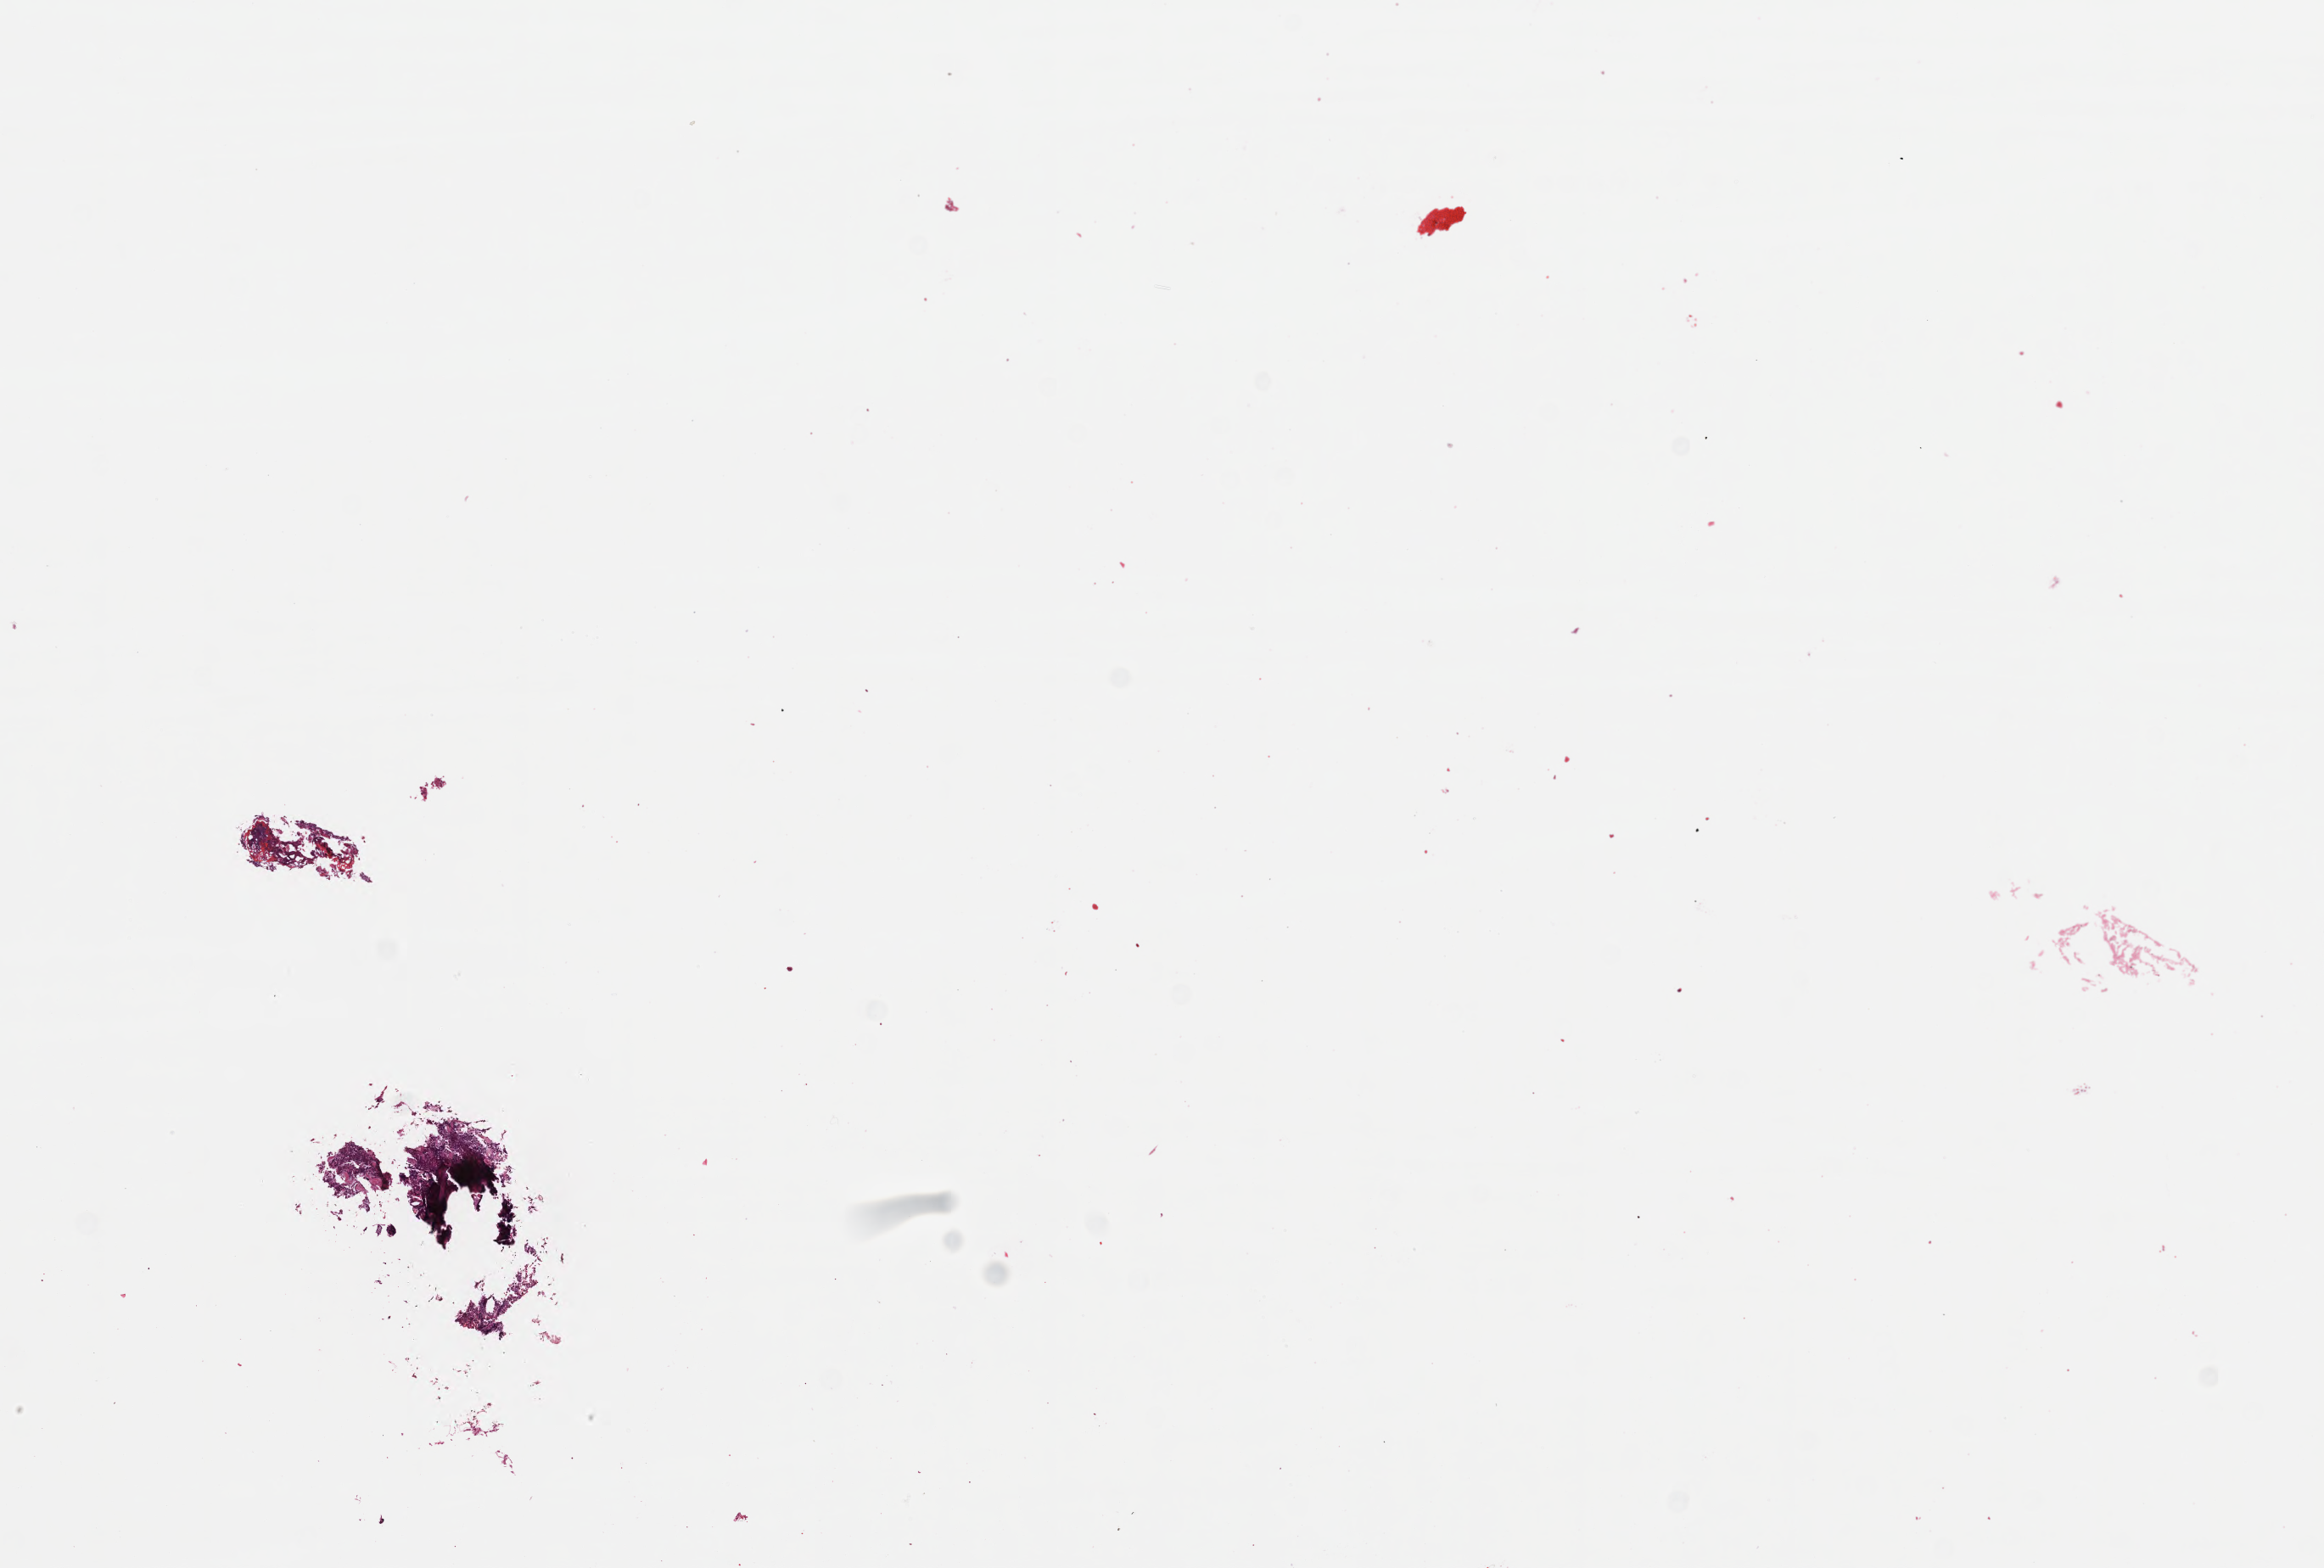
H&E whole-slide image, whole scanned area (about 11.1 x 7.5 mm) shown as a low-resolution overview. Formalin-fixed, paraffin-embedded (FFPE) tissue. Primary tumor. Patient male; aged 23.
Histologic diagnosis: Burkitt lymphoma, NOS.